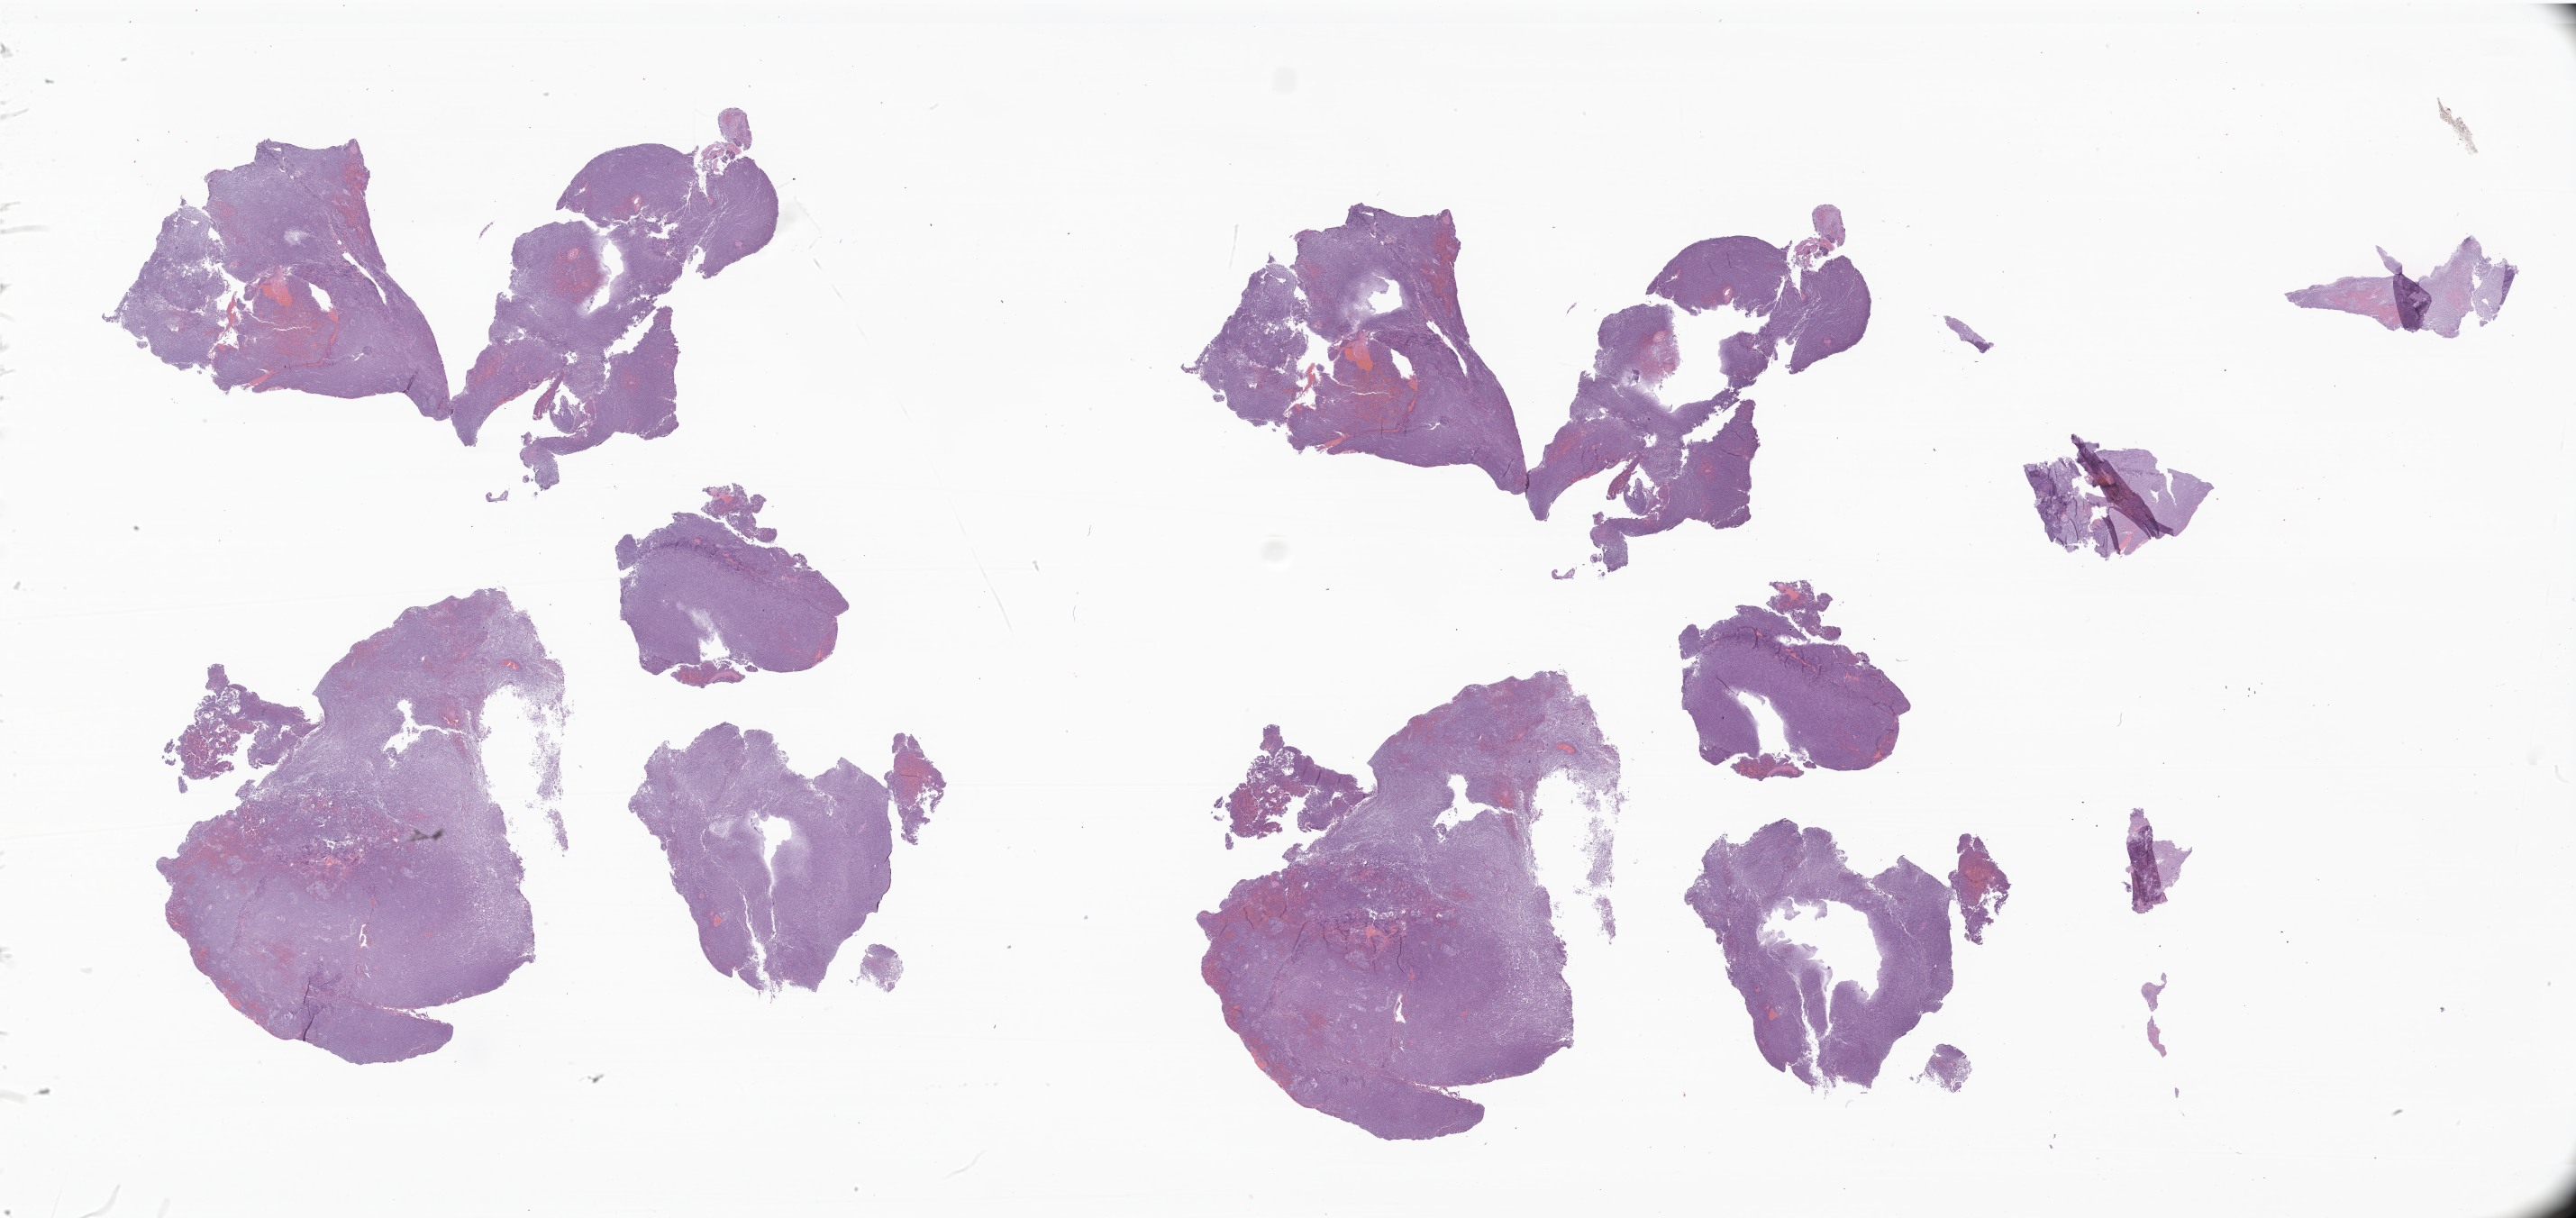
H&E whole-slide image of tumor tissue from the brain — a low-resolution overview of the entire scanned area, about 48.2 x 22.8 mm. FFPE section. Patient male; age 231 months (19 years 3 months).
Diagnosis (ICD-O-3 morphology term): Desmoplastic nodular medulloblastoma.